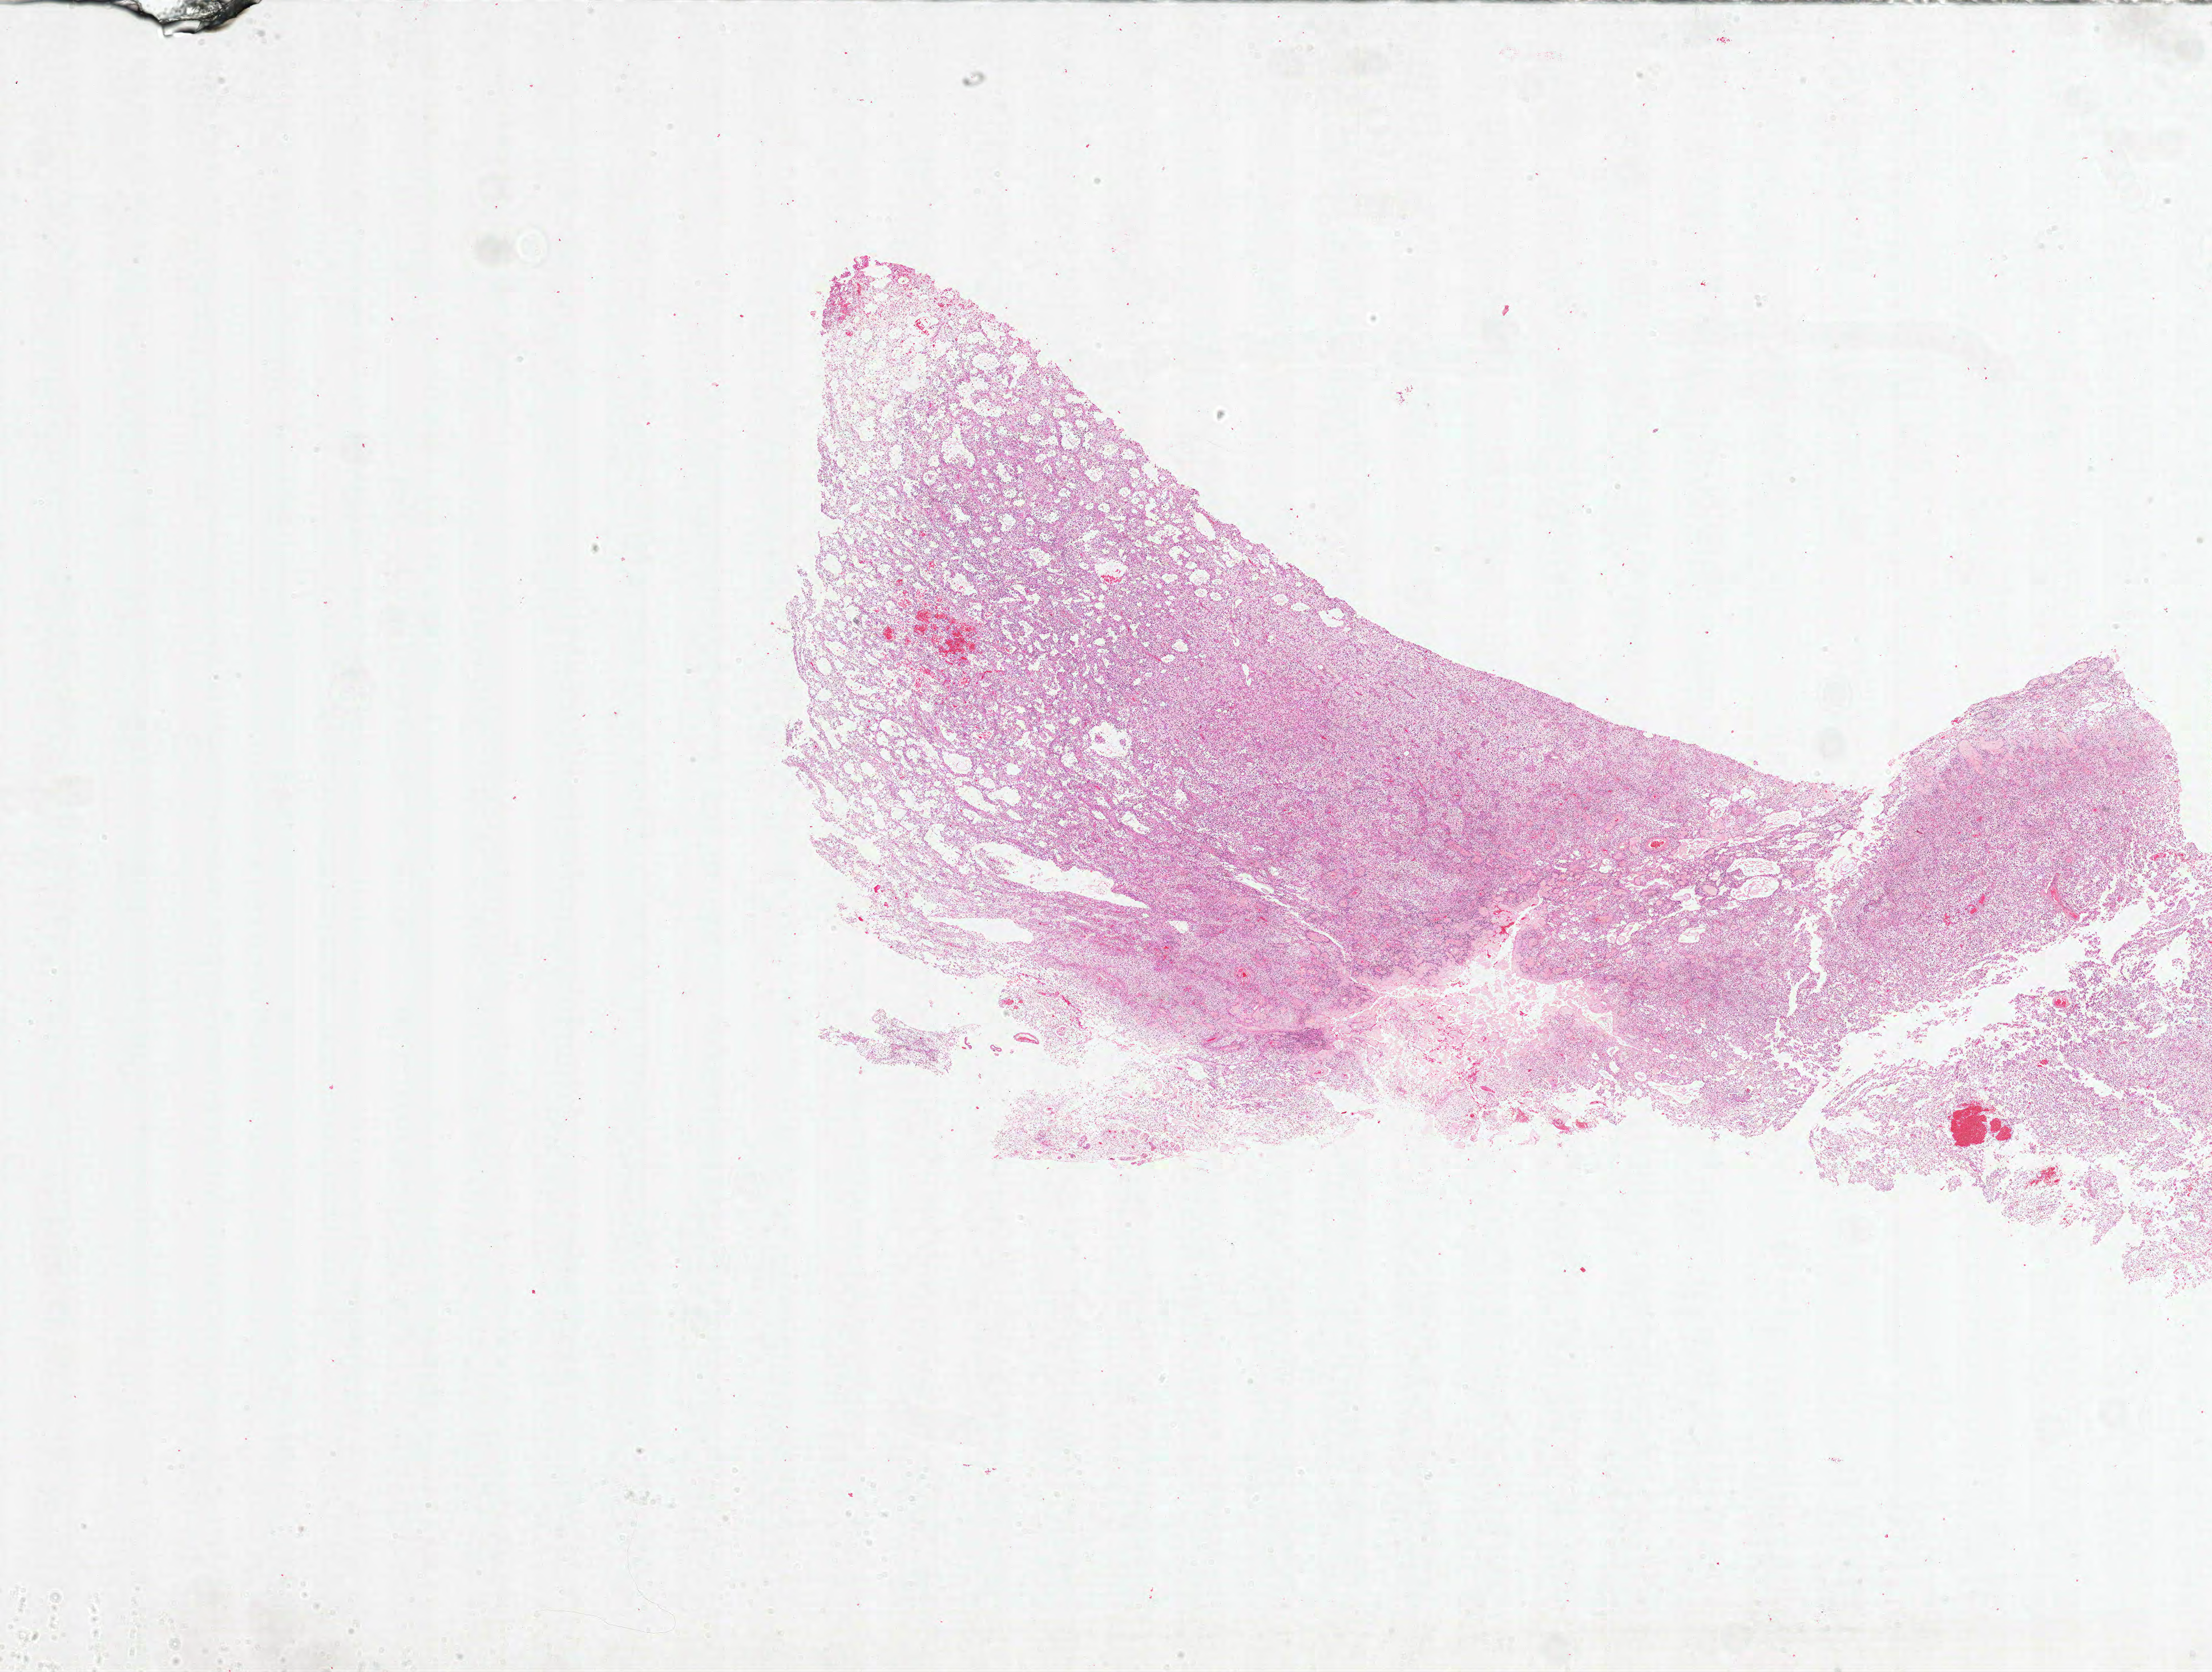
Digitized H&E-stained tissue section (whole slide), low-resolution overview of the scanned area, about 31.0 x 23.4 mm (slide scanned at 20x); FFPE section; sample: primary tumour, brain. Female, age 45 years at initial diagnosis.
Pathologic diagnosis: Glioblastoma.